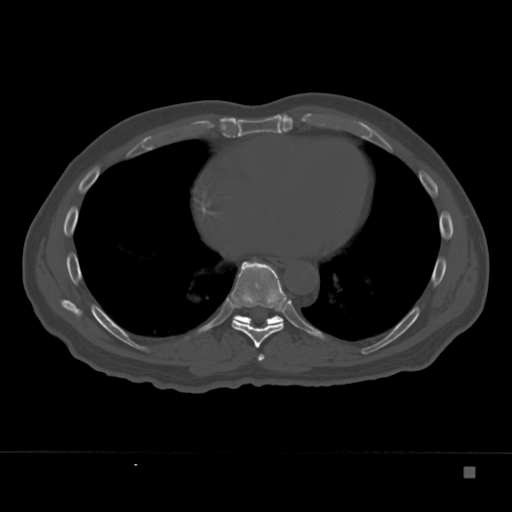
CT including the spine, one axial slice. Slice 202 of 332 in the series (ordered by position). Reconstruction kernel Br40s. 120 kVp. Bone window (W 1800 / L 400 HU). 512 × 512 image matrix. Male patient, age 72 years. From the clinical record (not read from this slice): primary cancer: skeletal.
Annotated regions visible in this slice (semi-automatically segmented with operator editing):
- T7 vertebra: bounding box <258,354,265,361> (left, top, right, bottom; pixels)
- T8 vertebra: <231,258,288,348>
- T9 vertebra: <232,315,284,328>